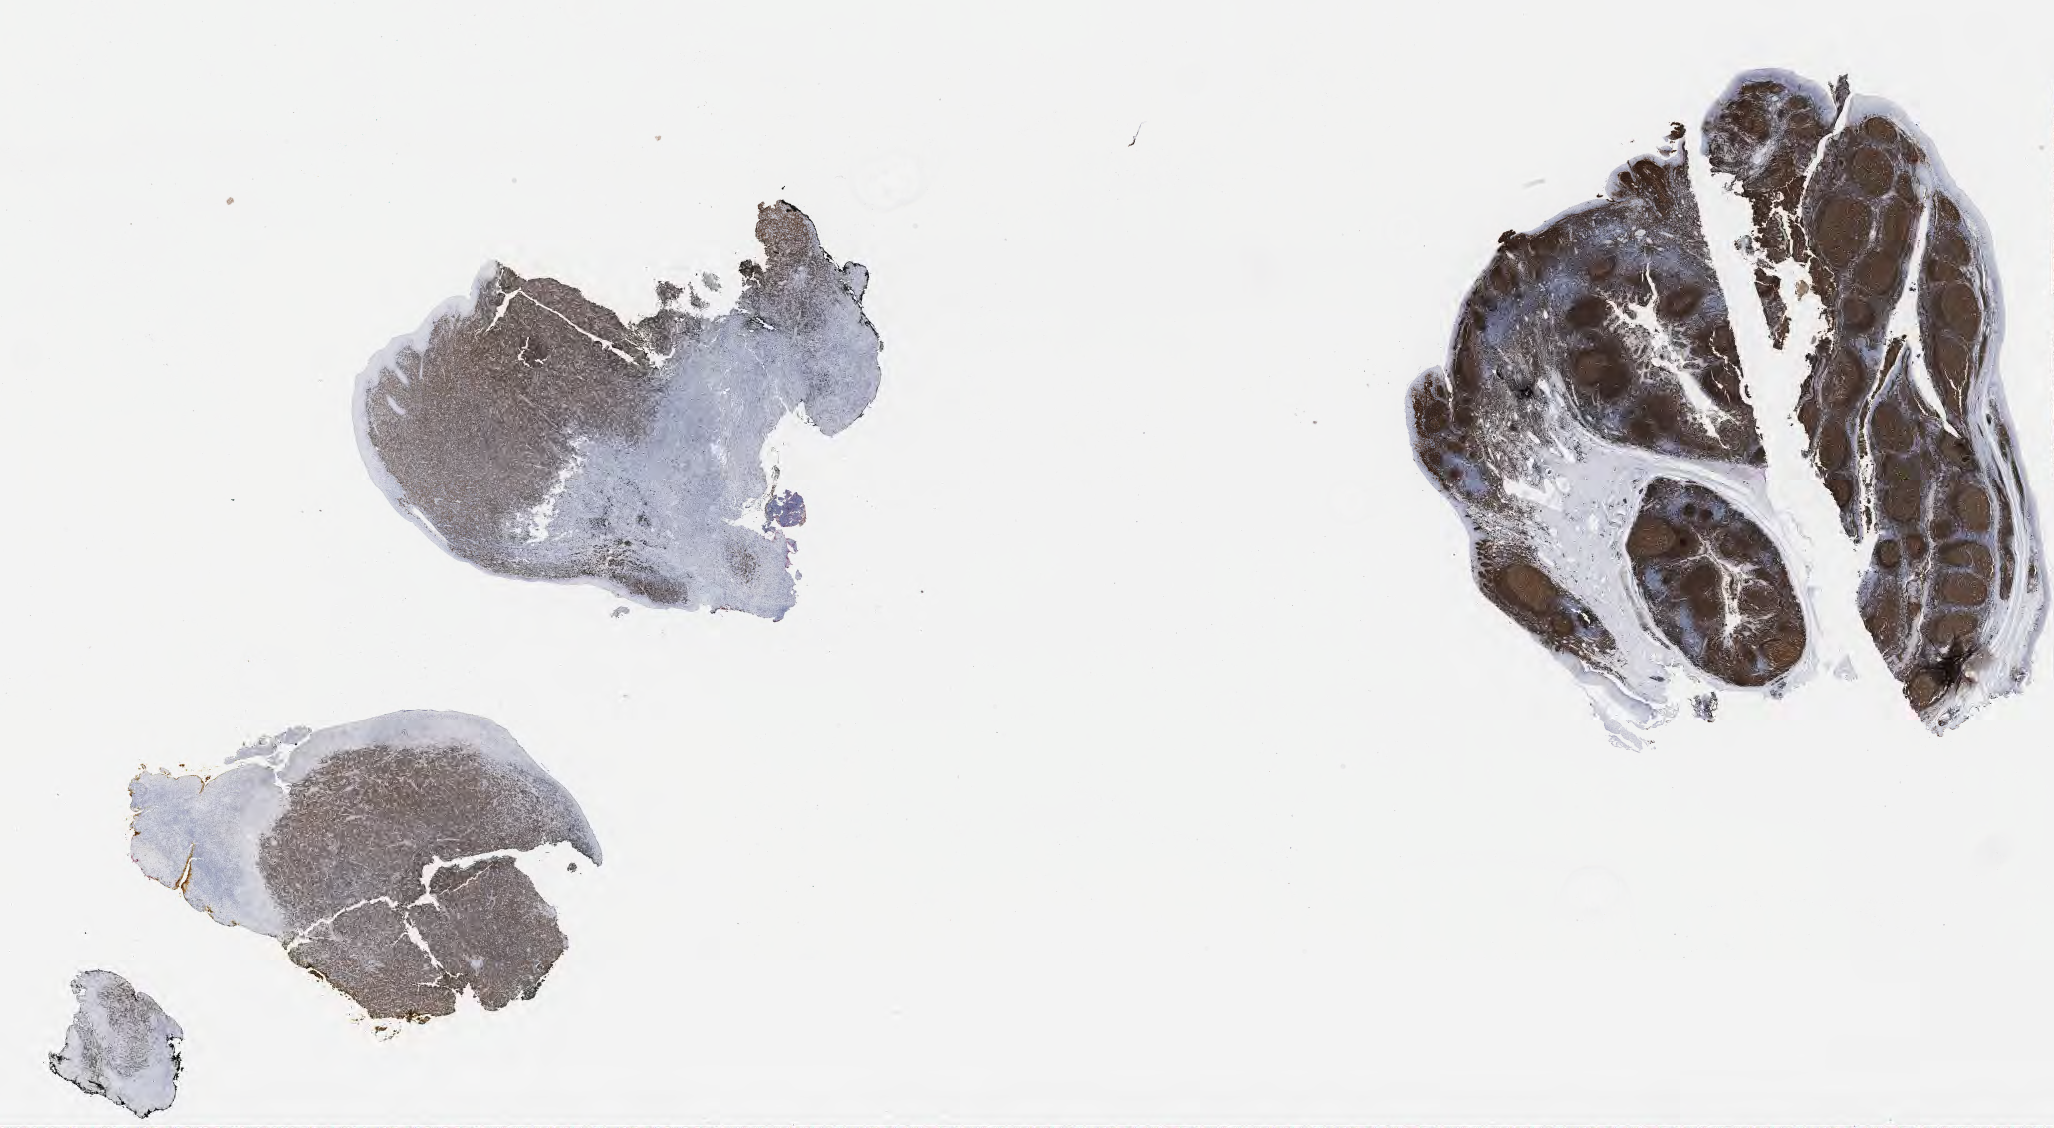
Immunohistochemistry (IHC) whole-slide image stained for CD79a — a low-resolution overview of the entire scanned area, about 33.2 x 18.2 mm, specimen: tumor tissue. Patient: male, 49 years old.
Histologic diagnosis: Diffuse large B-cell lymphoma, NOS.